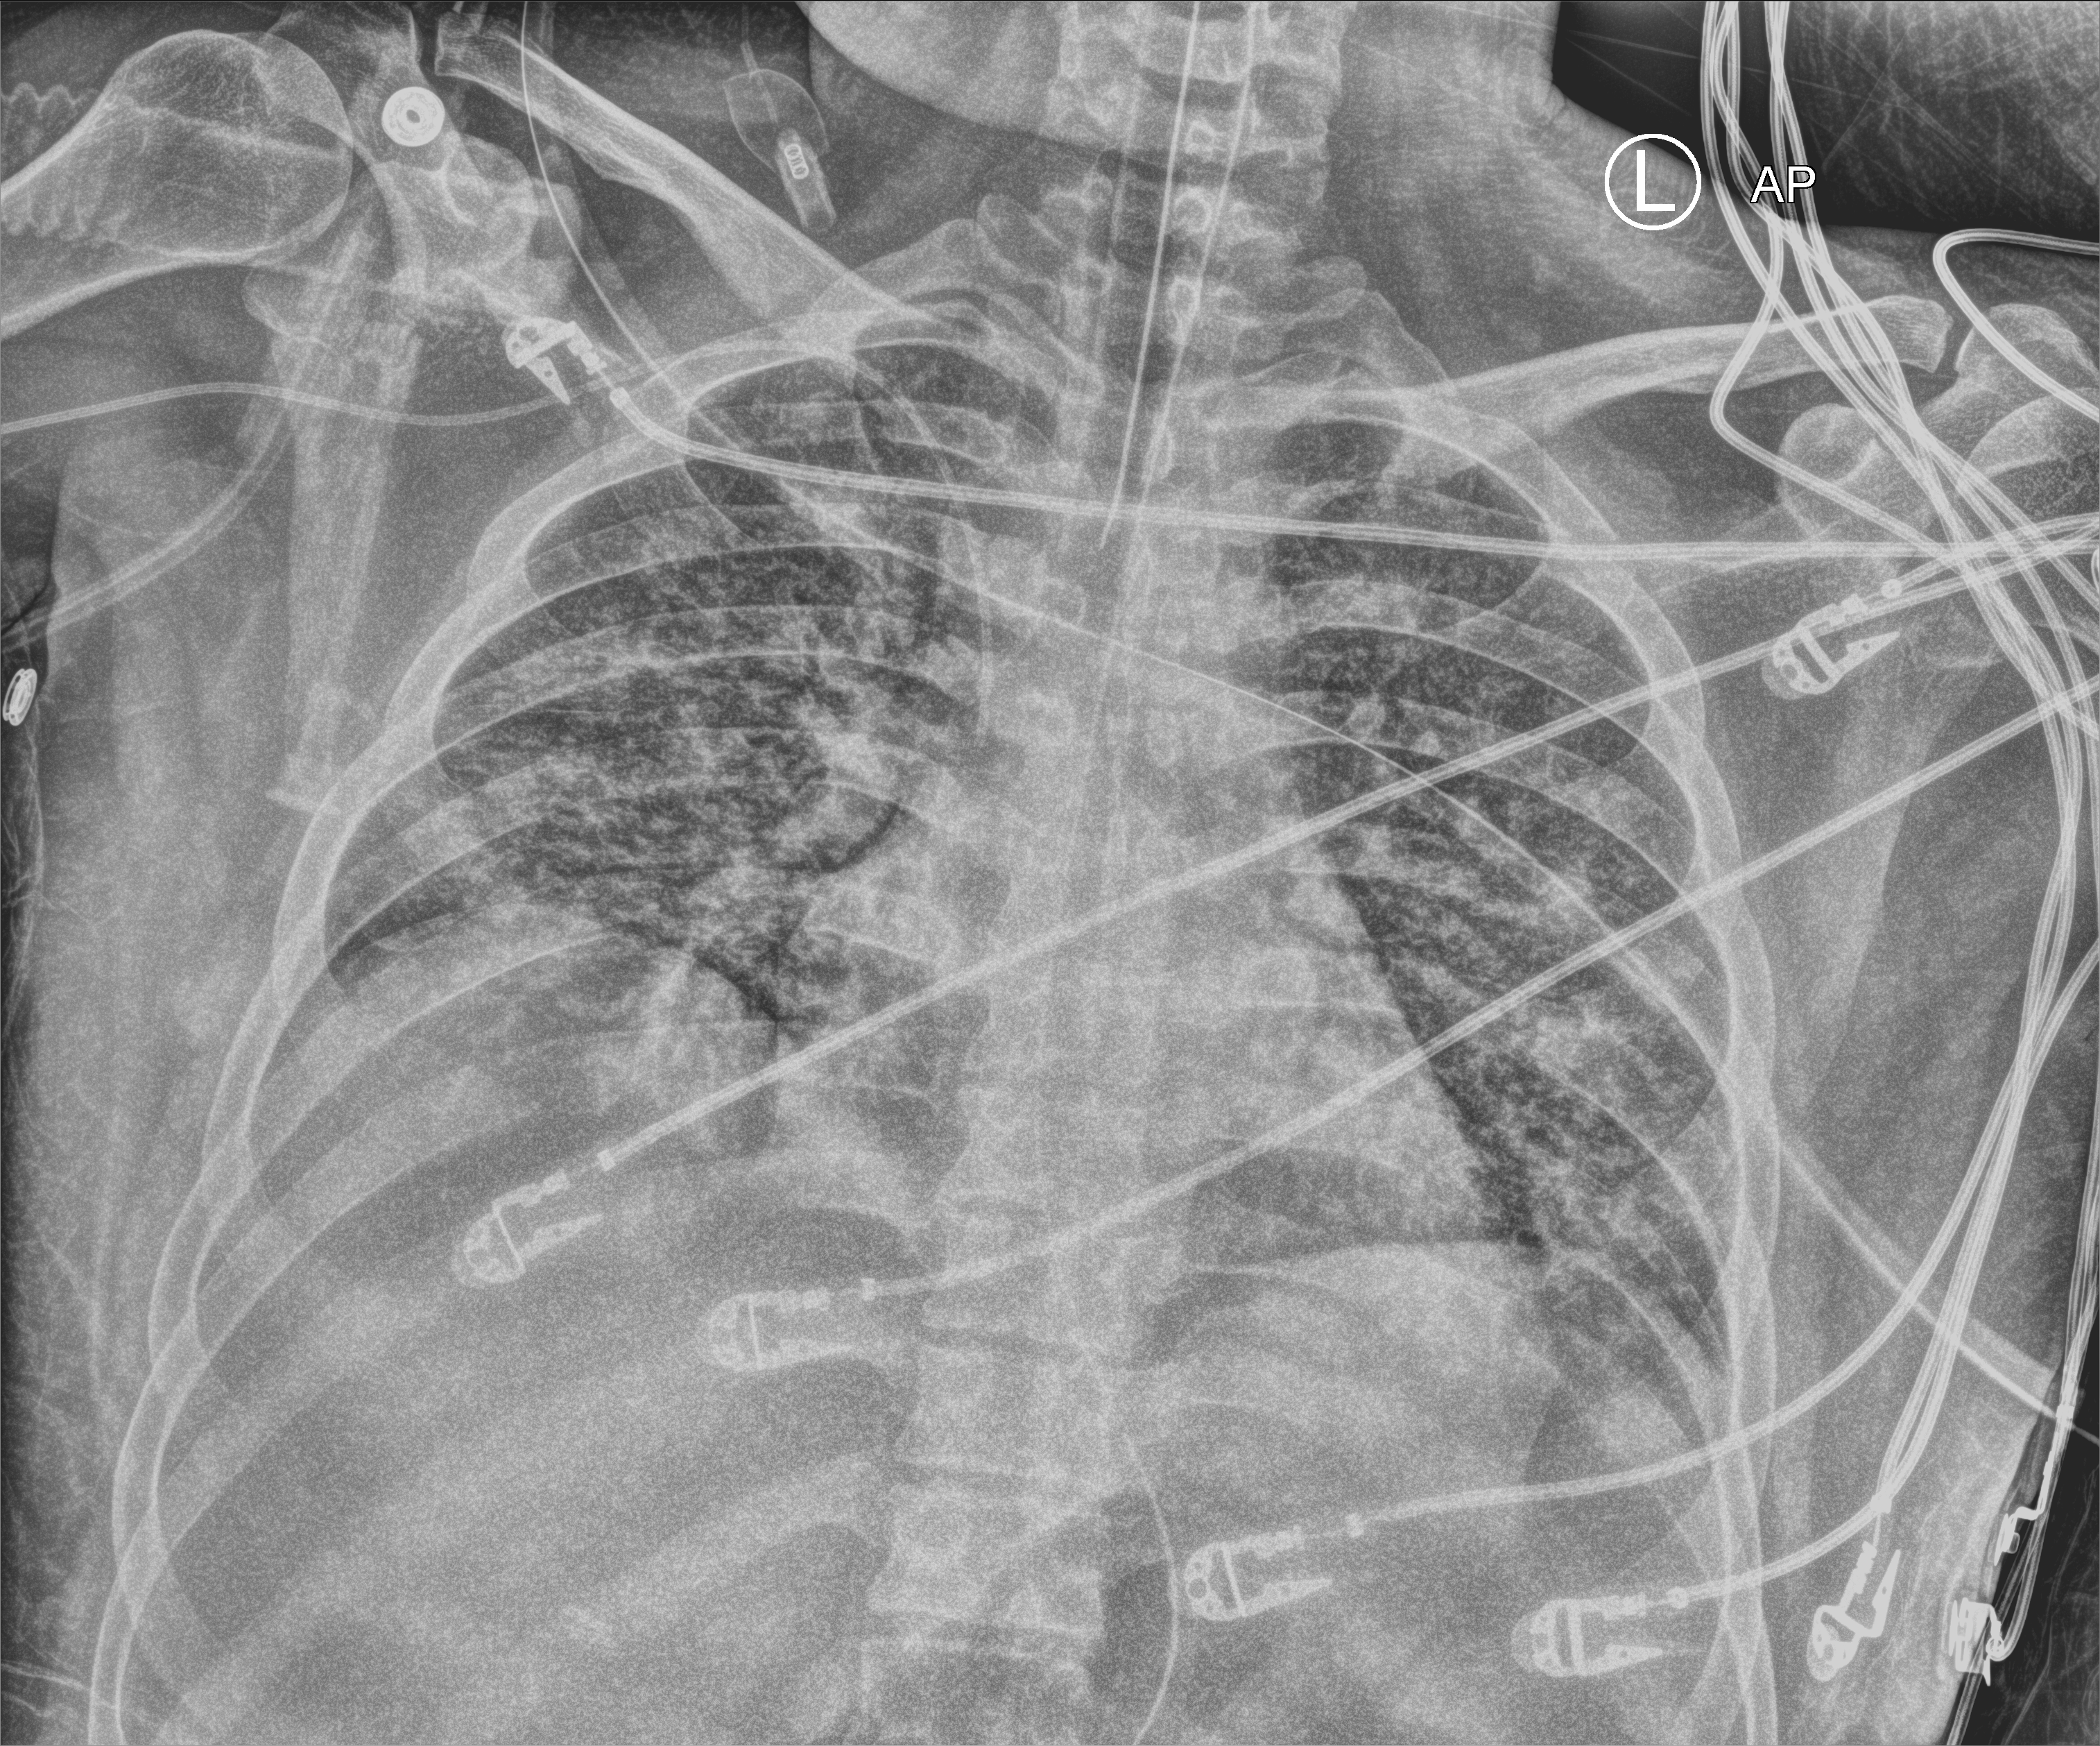
Portable chest radiograph; anteroposterior (AP) projection. Patient hospitalised with COVID-19; male, aged 18–59 years.
Admission-level facts for this patient (not findings on this image; timing relative to this image not recorded):
- admitted to intensive care during this hospital stay: yes
- chronic kidney disease (admission record): no
- mechanically ventilated during this hospital stay: yes